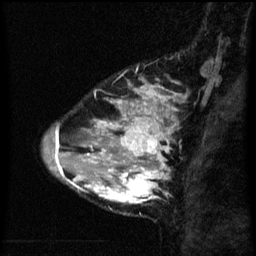
Breast MRI (dynamic contrast-enhanced), one sagittal slice. Slice 17 of 60 in the series (ordered by position). Dynamic contrast-enhanced series, image 2 of 3 at this slice position (ordered by acquisition). 1.5 T. TE 4.2 ms, TR 8 ms. 2.3 mm slice thickness. 256 × 256 image matrix. Female patient, age 33 years.
Structures marked on this image (semi-automatic segmentation, software-assisted and operator-edited):
- analysis volume of interest (the breast-tissue region the enhancement analysis was run in; not a lesion): bounding box <71,118,171,205> (left, top, right, bottom; pixels)
- tumour enhancement mask (voxels above the 70 % enhancement threshold inside the analysis volume of interest): <73,118,170,205>